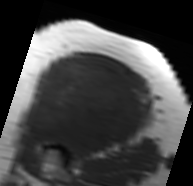
MRI of an extremity soft-tissue mass, one axial slice. Slice 49 of 91 in the series (ordered by position). MR volume resampled by the dataset authors to the PET/CT grid (not the native acquisition matrix). 193 × 186 image matrix, field of view 188 × 182 mm. Female patient. From the clinical record (not read from this slice): histological type: malignant solitary fibrous tumor; grade: intermediate; site of the primary tumour: right thigh.
Outlined on this slice (expert contour drawn on MRI and transferred to this co-registered scan by the dataset authors):
- gross tumour volume including surrounding oedema: box from (x=19, y=56) to (x=148, y=152) px
- gross tumour volume (mass): (x=24, y=56)–(x=146, y=150)